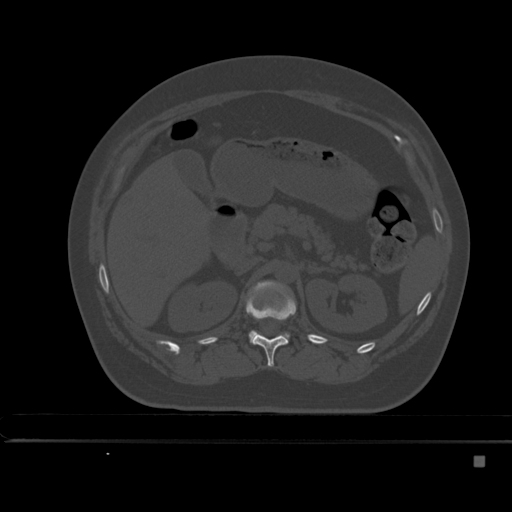
CT including the spine, one axial slice; position 207 of 495 along the scan axis; bone window (W 1800 / L 400 HU); 512 × 512 image matrix. Patient: female, 33 years. From the clinical record (not read from this slice): primary cancer: breast; vertebrae with lytic lesions (as recorded): T1.
Annotated regions visible in this slice (semi-automatically segmented with operator editing):
- L1 vertebra: box from (x=249, y=281) to (x=289, y=342) px
- T12 vertebra: (x=246, y=285)–(x=296, y=367)